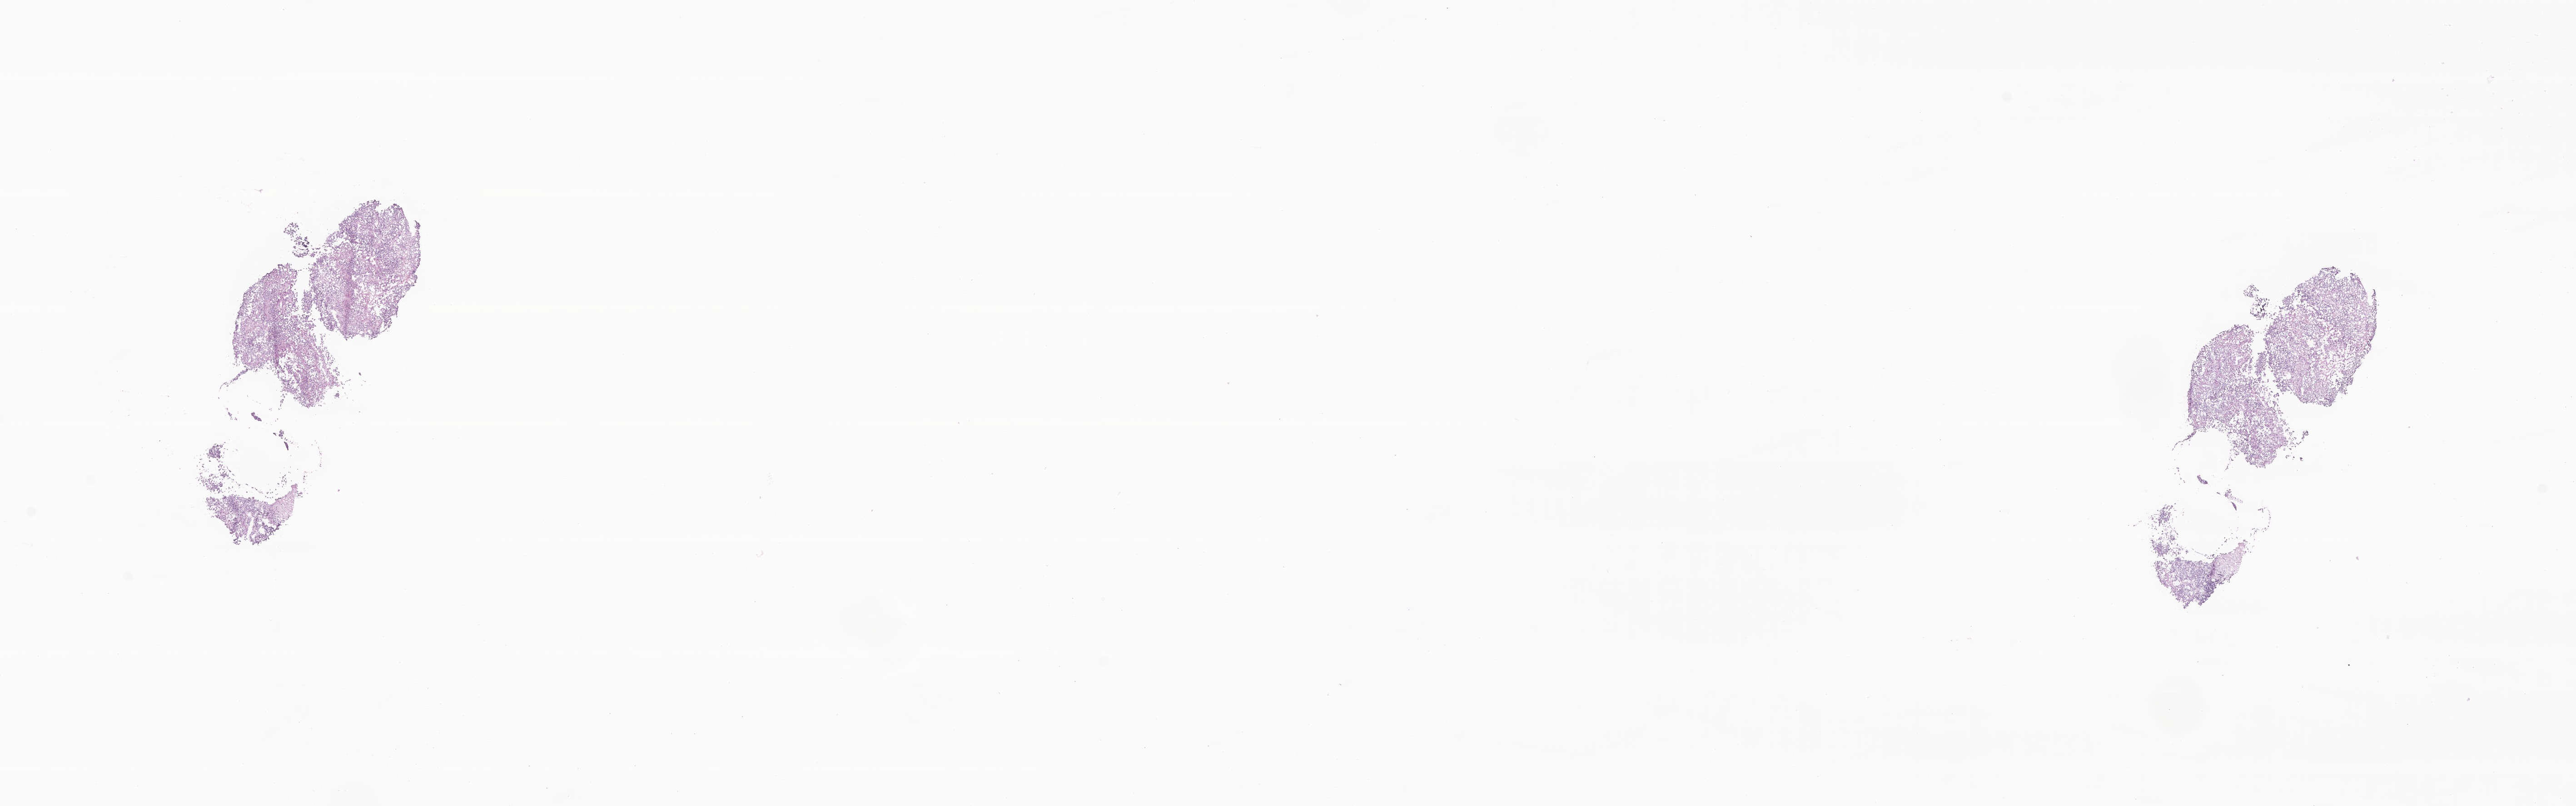
Whole-slide image, haematoxylin and eosin stain of tumor tissue from the pelvis, shown as a low-resolution overview of the whole scanned area (about 23.9 x 7.5 mm); frozen section. Patient female; age 212 months.
Diagnosis (ICD-O-3 morphology term): Rhabdomyosarcoma, NOS.